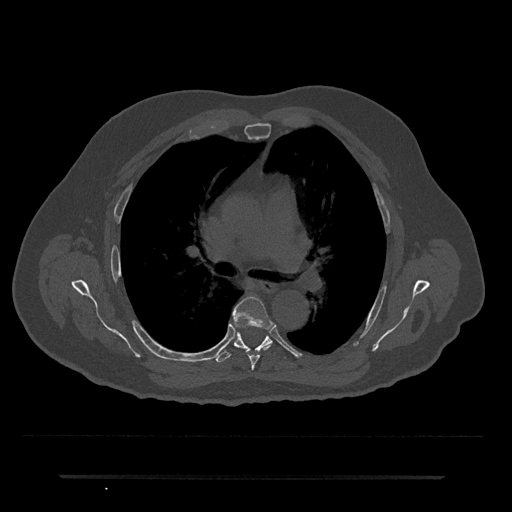
CT including the spine, one axial slice. Position 461 of 797 along the scan axis. 120 kVp. Bone window (W 1800 / L 400 HU). 512 × 512 image matrix. Patient: male, 69 years. From the clinical record (not read from this slice): primary cancer: prostate.
Outlined on this slice (semi-automatically segmented with operator editing):
- T5 vertebra: box from (x=233, y=296) to (x=273, y=370) px
- T6 vertebra: (x=216, y=321)–(x=272, y=363)